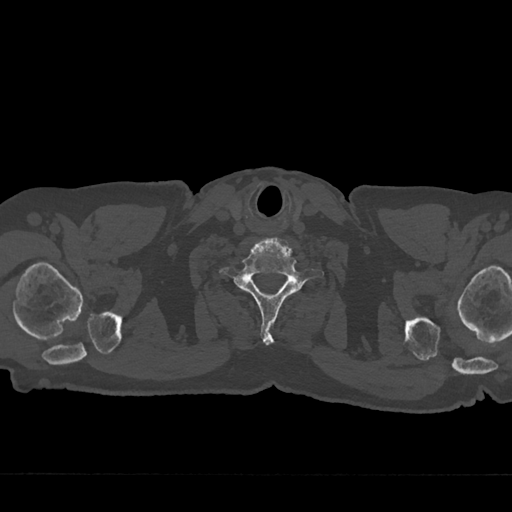
CT including the spine, one axial slice; position 691 of 797 along the scan axis; 120 kVp; bone window (W 1800 / L 400 HU); 0.5 mm slice thickness; 512 × 512 image matrix, field of view 377 × 377 mm. Male patient, age 75 years. Case-level facts recorded for this patient, not image findings: primary cancer: renal; vertebrae with lytic lesions (as recorded): T4.
Structures marked on this image (semi-automatic segmentation, software-assisted and operator-edited):
- T1 vertebra: bounding box (x1, y1, x2, y2) in pixels: (216, 285, 219, 287)